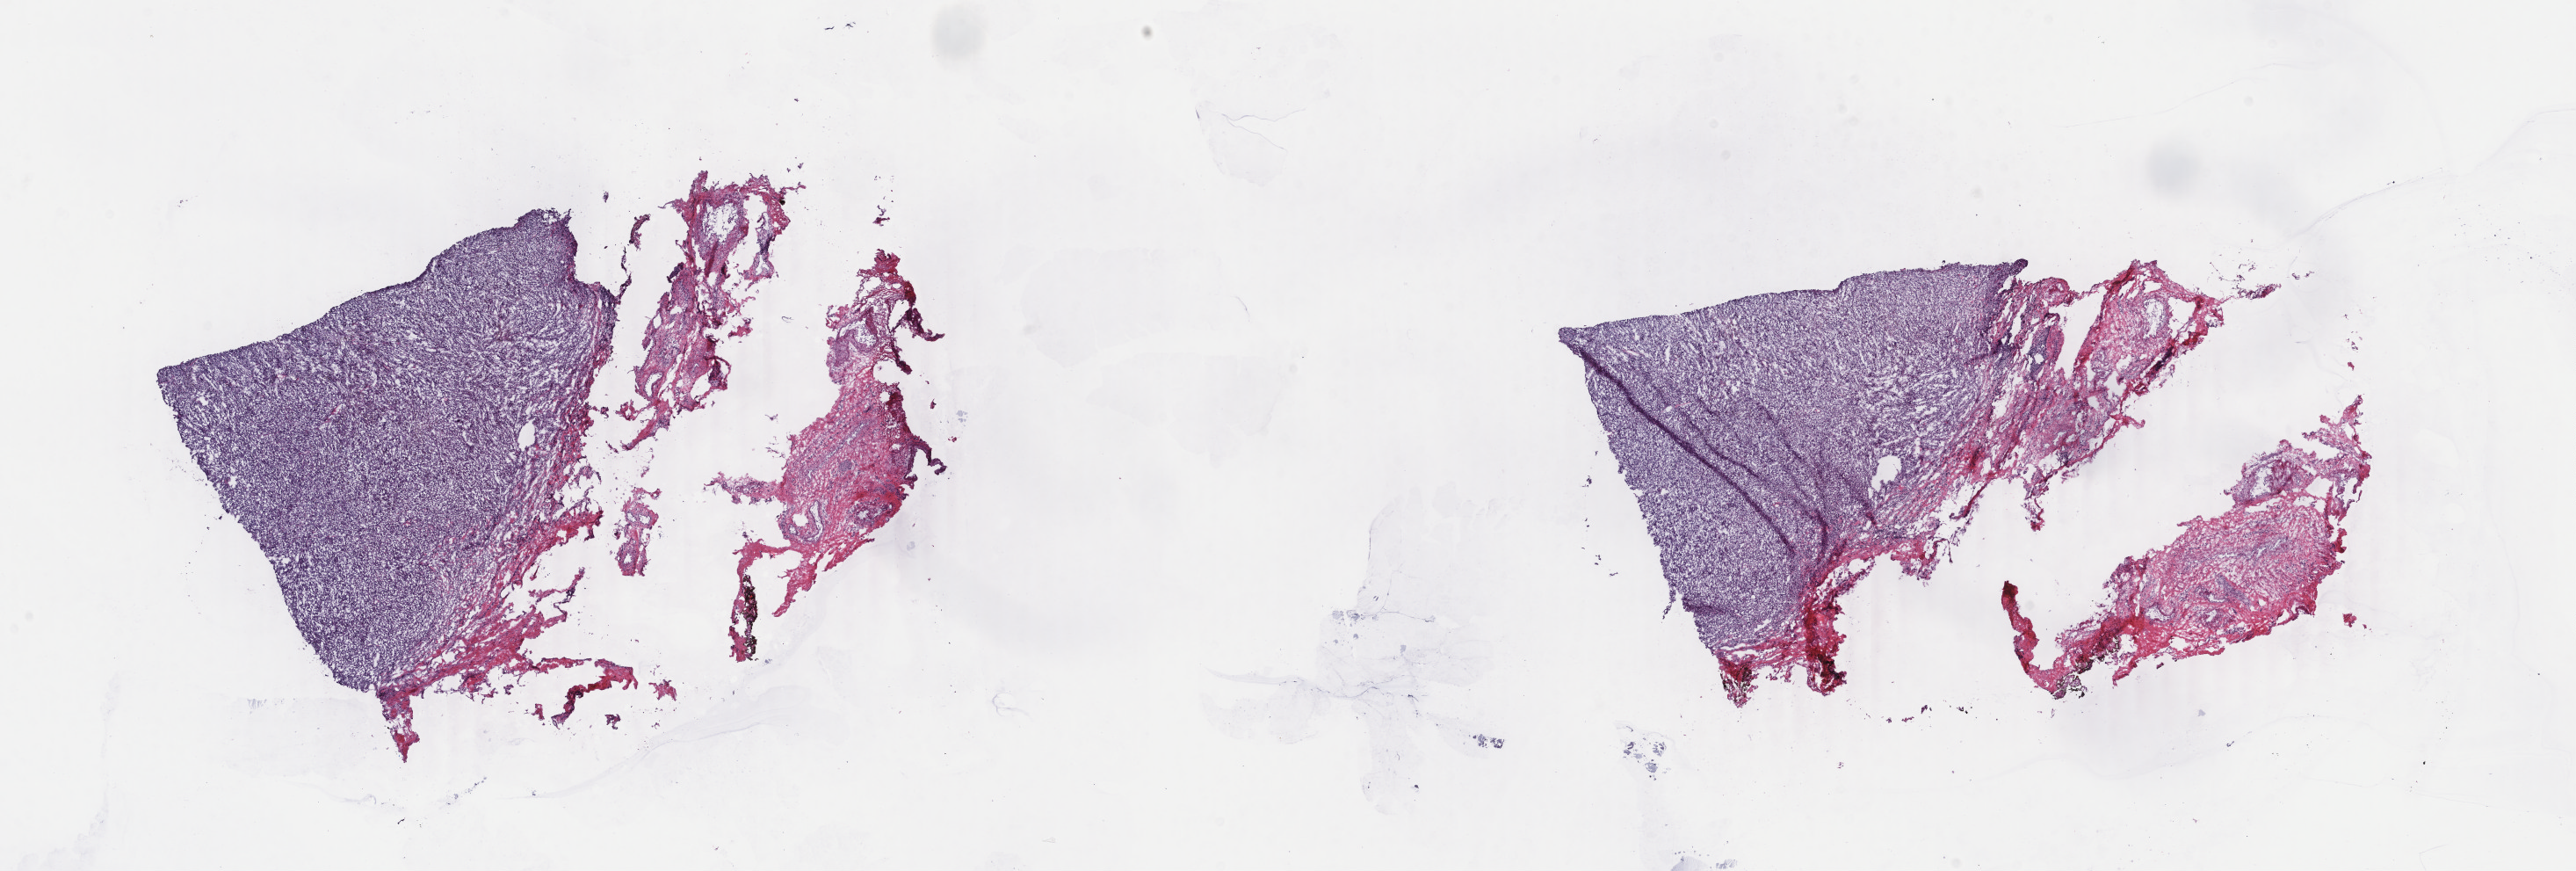
H&E-stained whole-slide image, whole scanned area (about 23.3 x 7.9 mm, acquisition: 40x scan) shown as a low-resolution overview; frozen section from the top of the tissue portion; metastatic tumour sample, sampled site not recorded. Patient: male, age at initial diagnosis 62 years. Composition of this section per pathologist review: tumour cells 75%, tumour nuclei 90%, normal cells 0%, stromal cells 25%, necrosis 0%. Infiltration values recorded for this section: lymphocyte infiltration 0%, monocyte infiltration 0%, neutrophil infiltration 0%.
- this section: metastatic tumour tissue
- patient diagnosis: Malignant melanoma, NOS